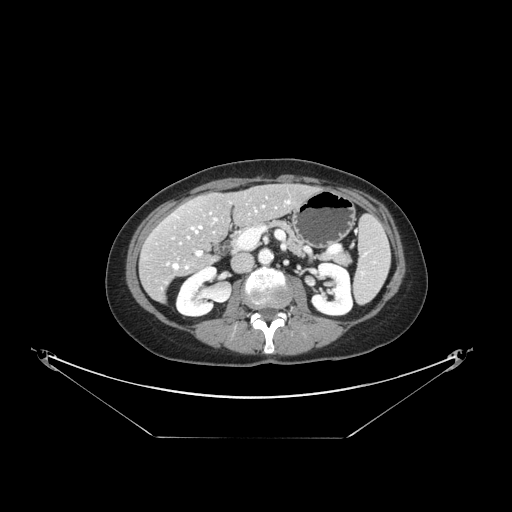
Contrast-enhanced abdominal CT, one axial slice. Slice 68 of 148 in the series (ordered by position). Reconstruction kernel STANDARD. 120 kVp. Intravenous contrast given. Soft-tissue window (W 400 / L 40 HU). 512 × 512 image matrix. Female patient, age 73 years. From the clinical record (not read from this slice): diagnosis: colorectal cancer liver metastases, imaged before liver resection; multiple liver metastases: no; largest metastasis: 1 cm; disease in both lobes: no.
Annotated regions visible in this slice (expert manual segmentation):
- hepatic veins: bounding box [x1, y1, x2, y2] px = [173, 200, 290, 269]
- liver: [141, 185, 314, 300]
- planned liver remnant (the part of the liver to remain after resection): [167, 185, 313, 249]
- portal vein (with intrahepatic branches): [196, 251, 201, 256]